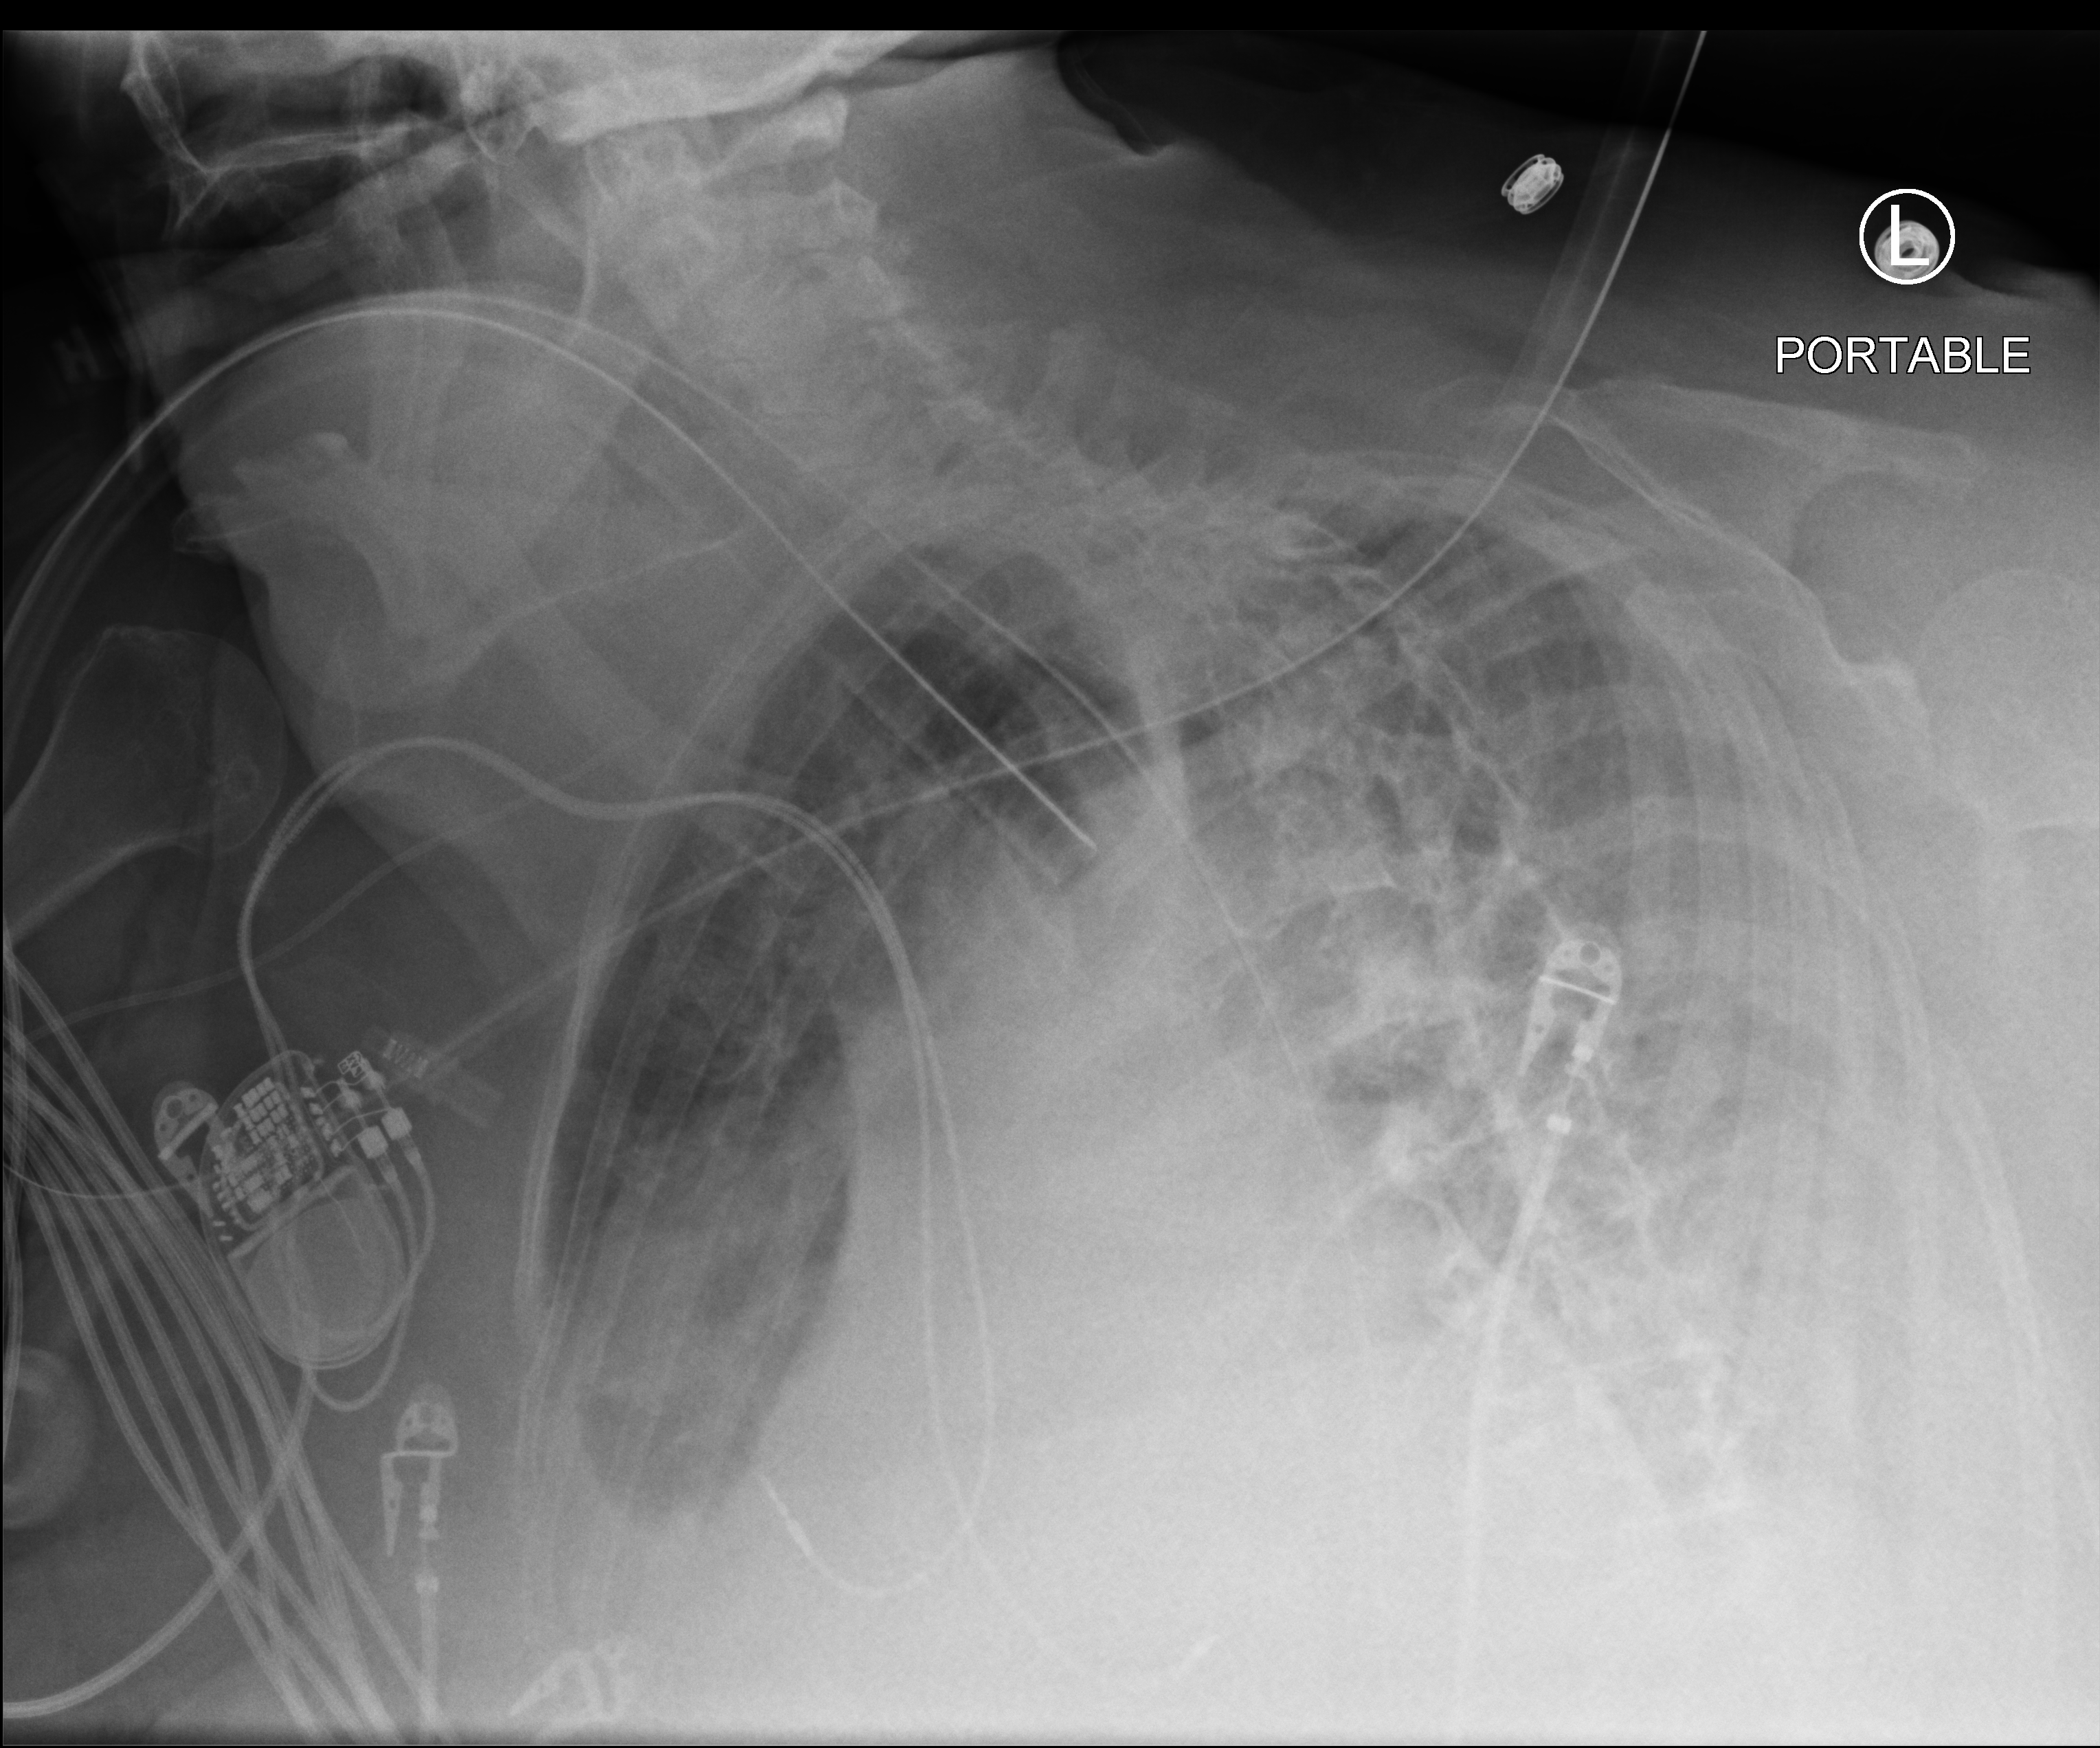
Portable chest radiograph; anteroposterior (AP) projection. Patient hospitalised with COVID-19; female, aged 75–90 years.
Admission-level facts for this patient (not findings on this image; timing relative to this image not recorded): hypertension (admission record): yes.